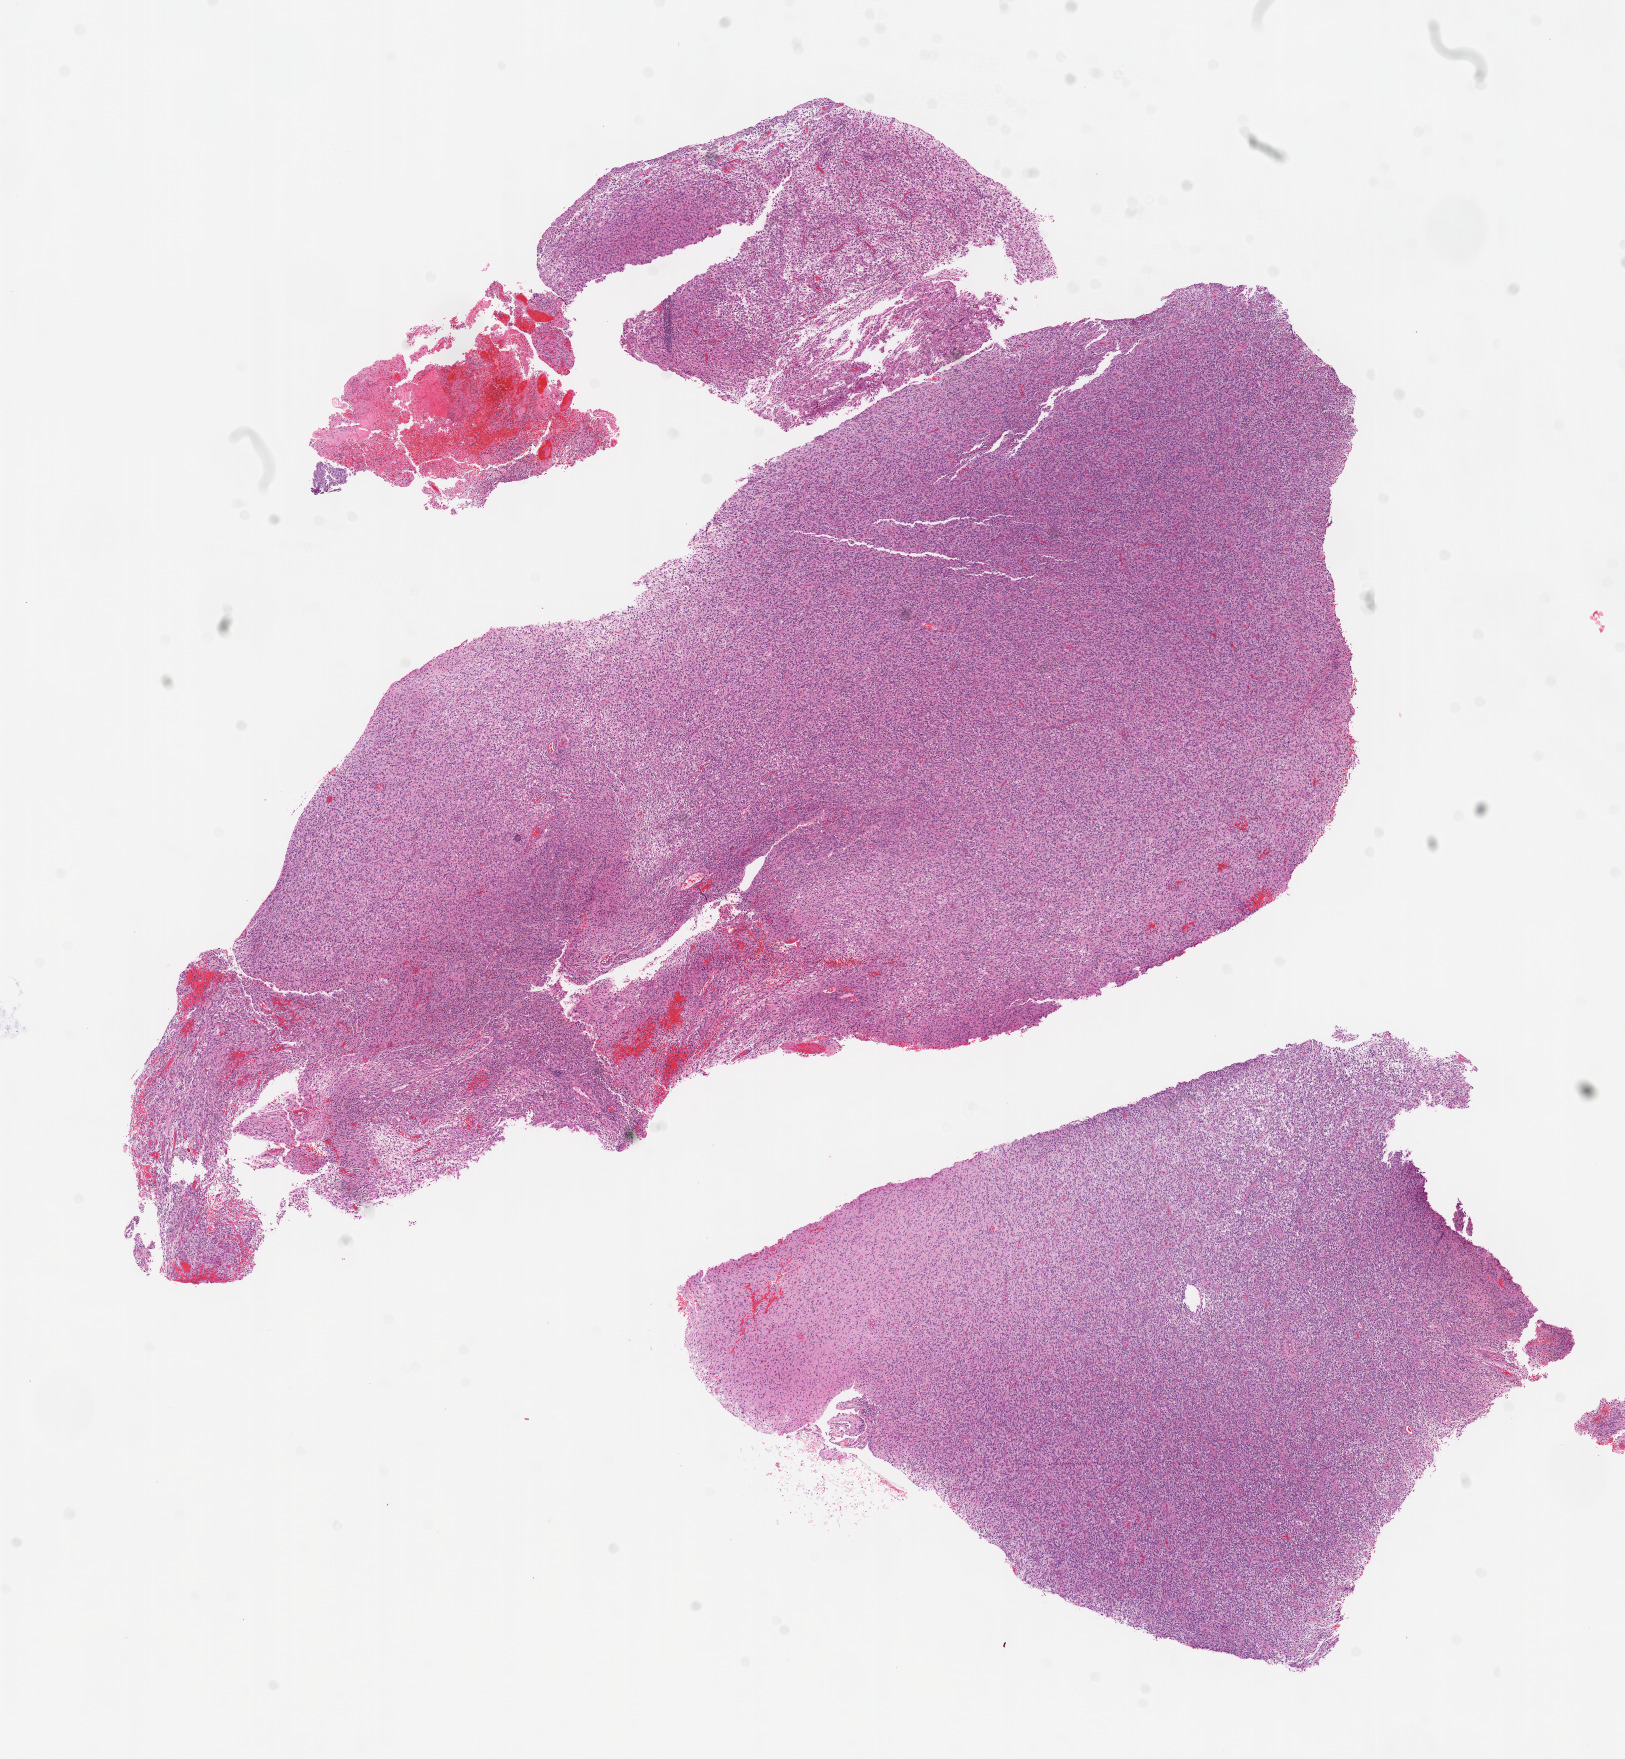
Whole-slide histology image, Hematoxylin and eosin (H&E) stained — a low-resolution overview of the entire scanned area, about 13.0 x 14.1 mm (slide scanned at 20x), frozen section from the top of the tissue portion, primary tumour sample from the brain. Male patient; age at initial diagnosis 52 years. Pathologist review of this section (percent, as recorded): tumour cells 100%, tumour nuclei 75%, normal cells 0%, stromal cells 0%, necrosis 0%.
Diagnosis: Glioblastoma.